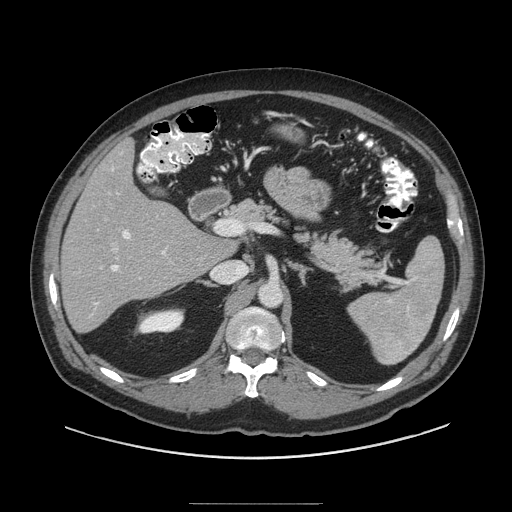
Contrast-enhanced abdominal CT (liver protocol), one axial slice. Slice 53 of 91 in the series (ordered by position). Soft-tissue window (W 400 / L 40 HU). 512 × 512 image matrix. Case-level facts recorded for this patient, not image findings: diagnosis: hepatocellular carcinoma (patient treated with transarterial chemoembolisation; whether this scan precedes or follows treatment is not stated here); TNM stage (as recorded): Stage-I; Child-Pugh class: A; tumour nodularity: uninodular; tumour size: 4 cm.
Annotated regions visible in this slice (semi-automatically segmented with operator editing):
- liver parenchyma outside the tumour (the mass and vessels are separate outlines, so this box may not span the whole liver): bounding box [x1, y1, x2, y2] px = [60, 138, 234, 332]
- liver vessels: [95, 168, 166, 305]